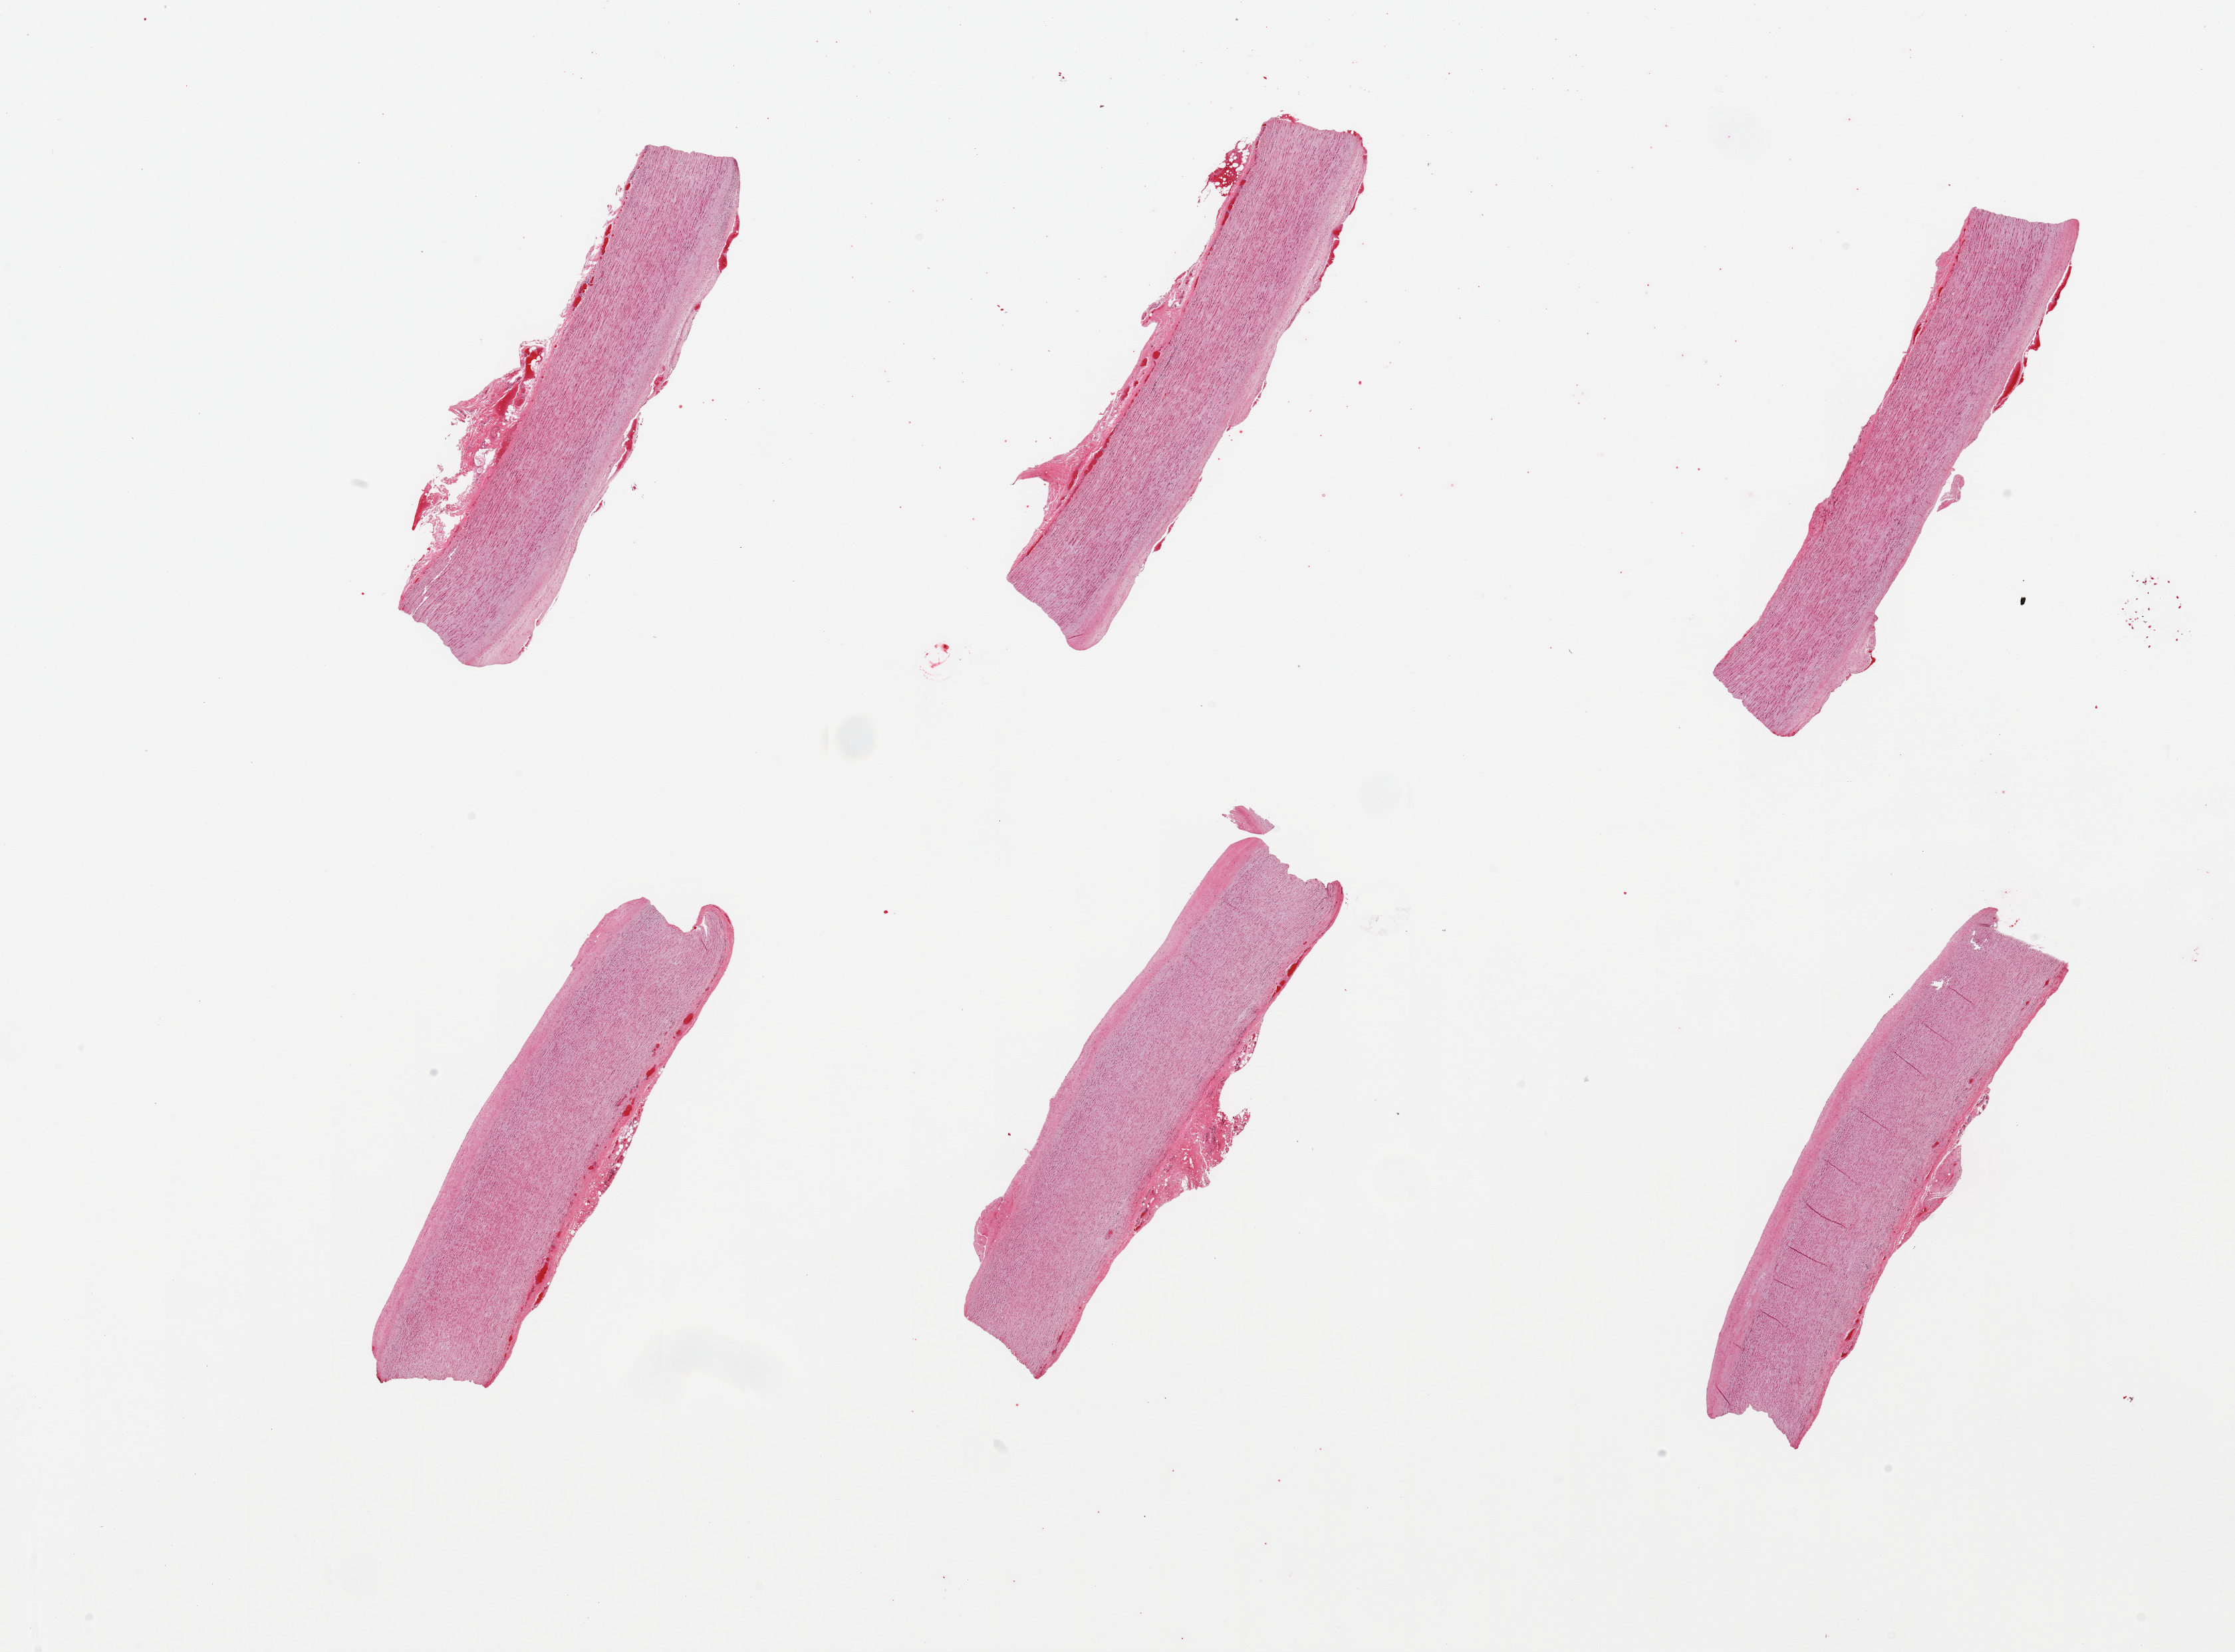
Haematoxylin and eosin whole-slide image — shown as a low-resolution overview of the whole scanned area (about 26.6 x 19.7 mm, acquisition: 20x scan). PAXgene-fixed, paraffin-embedded tissue. Section of aorta (target tissue). Donor tissue sample. Male donor.
- review note (as recorded): 6 pieces; atheromatous plaques; congested adventitia